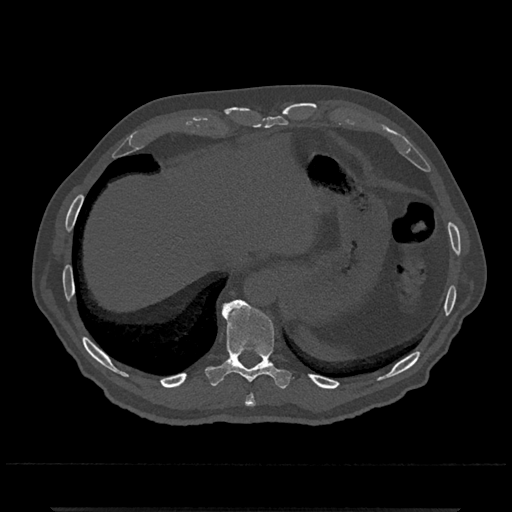
CT including the spine, one axial slice. Position 555 of 797 along the scan axis. Reconstruction kernel Br40s/3. 120 kVp. Bone window (W 1800 / L 400 HU). 512 × 512 image matrix, field of view 393 × 393 mm. Male patient, age 67 years. Case-level facts recorded for this patient, not image findings: primary cancer: prostate.
Outlined on this slice (semi-automatic segmentation, software-assisted and operator-edited):
- T10 vertebra: bounding box (x1, y1, x2, y2) in pixels: (204, 299, 292, 389)
- T9 vertebra: (245, 394, 256, 407)